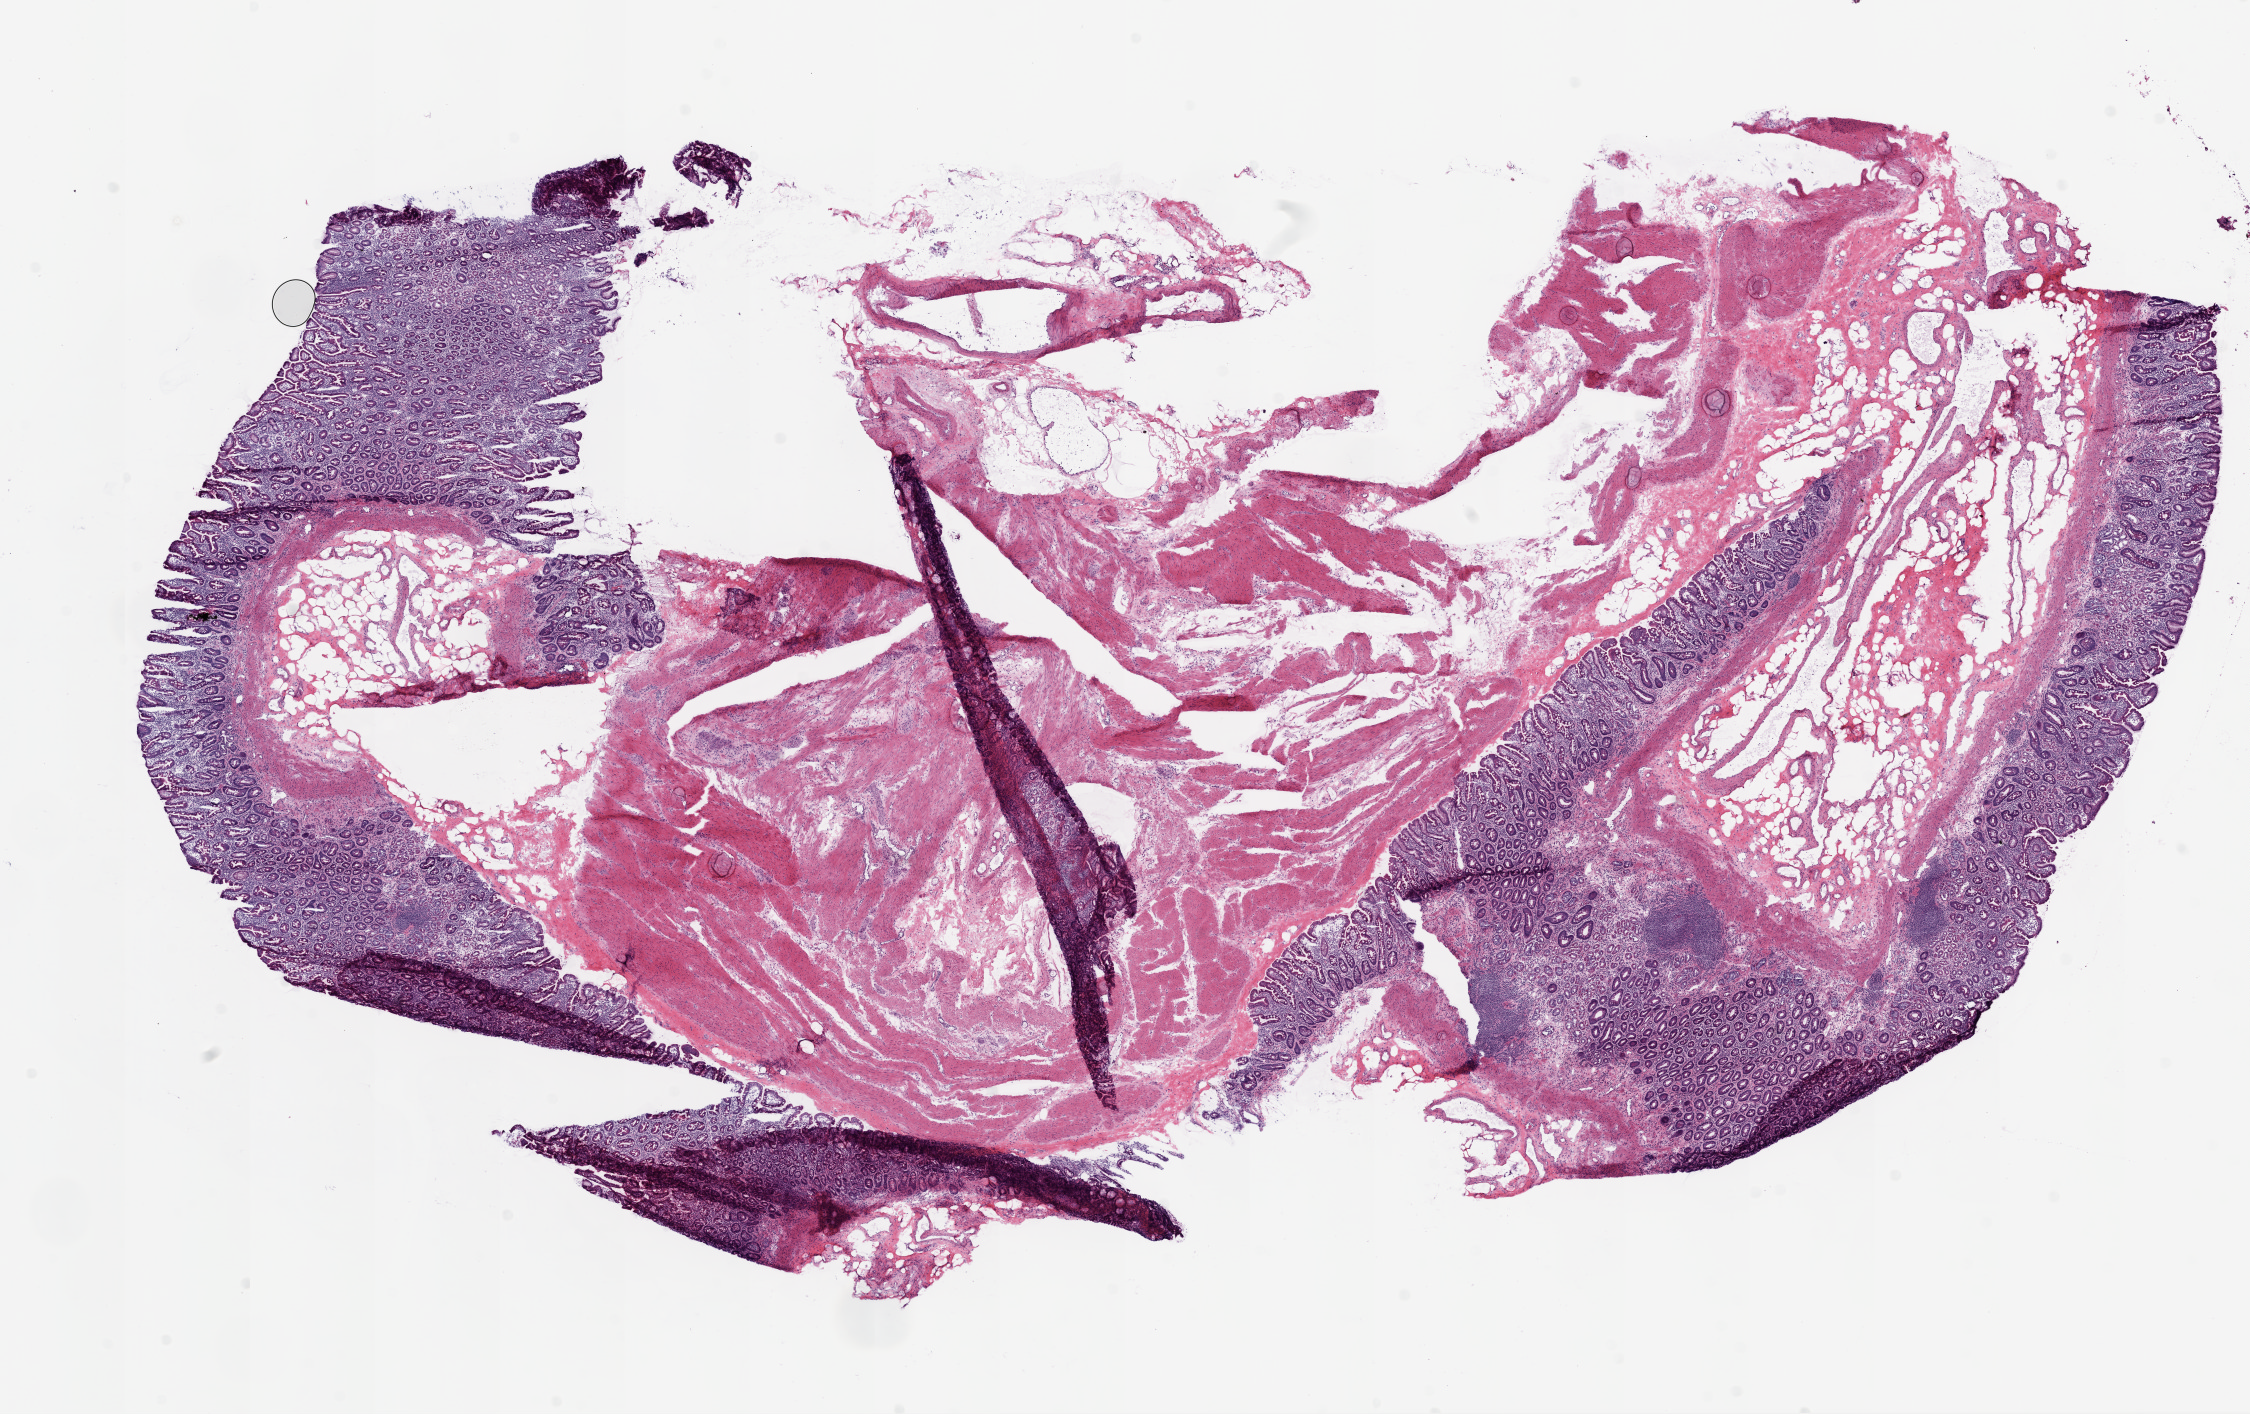
H&E-stained whole-slide image — a low-resolution overview of the entire scanned area, about 18.1 x 11.3 mm, frozen section, stomach, solid tissue normal (non-tumour tissue) sample. Female patient; age at initial diagnosis 71 years.
This section: solid tissue normal sample (biorepository sample class). Patient diagnosis: Adenocarcinoma, NOS (body of stomach).